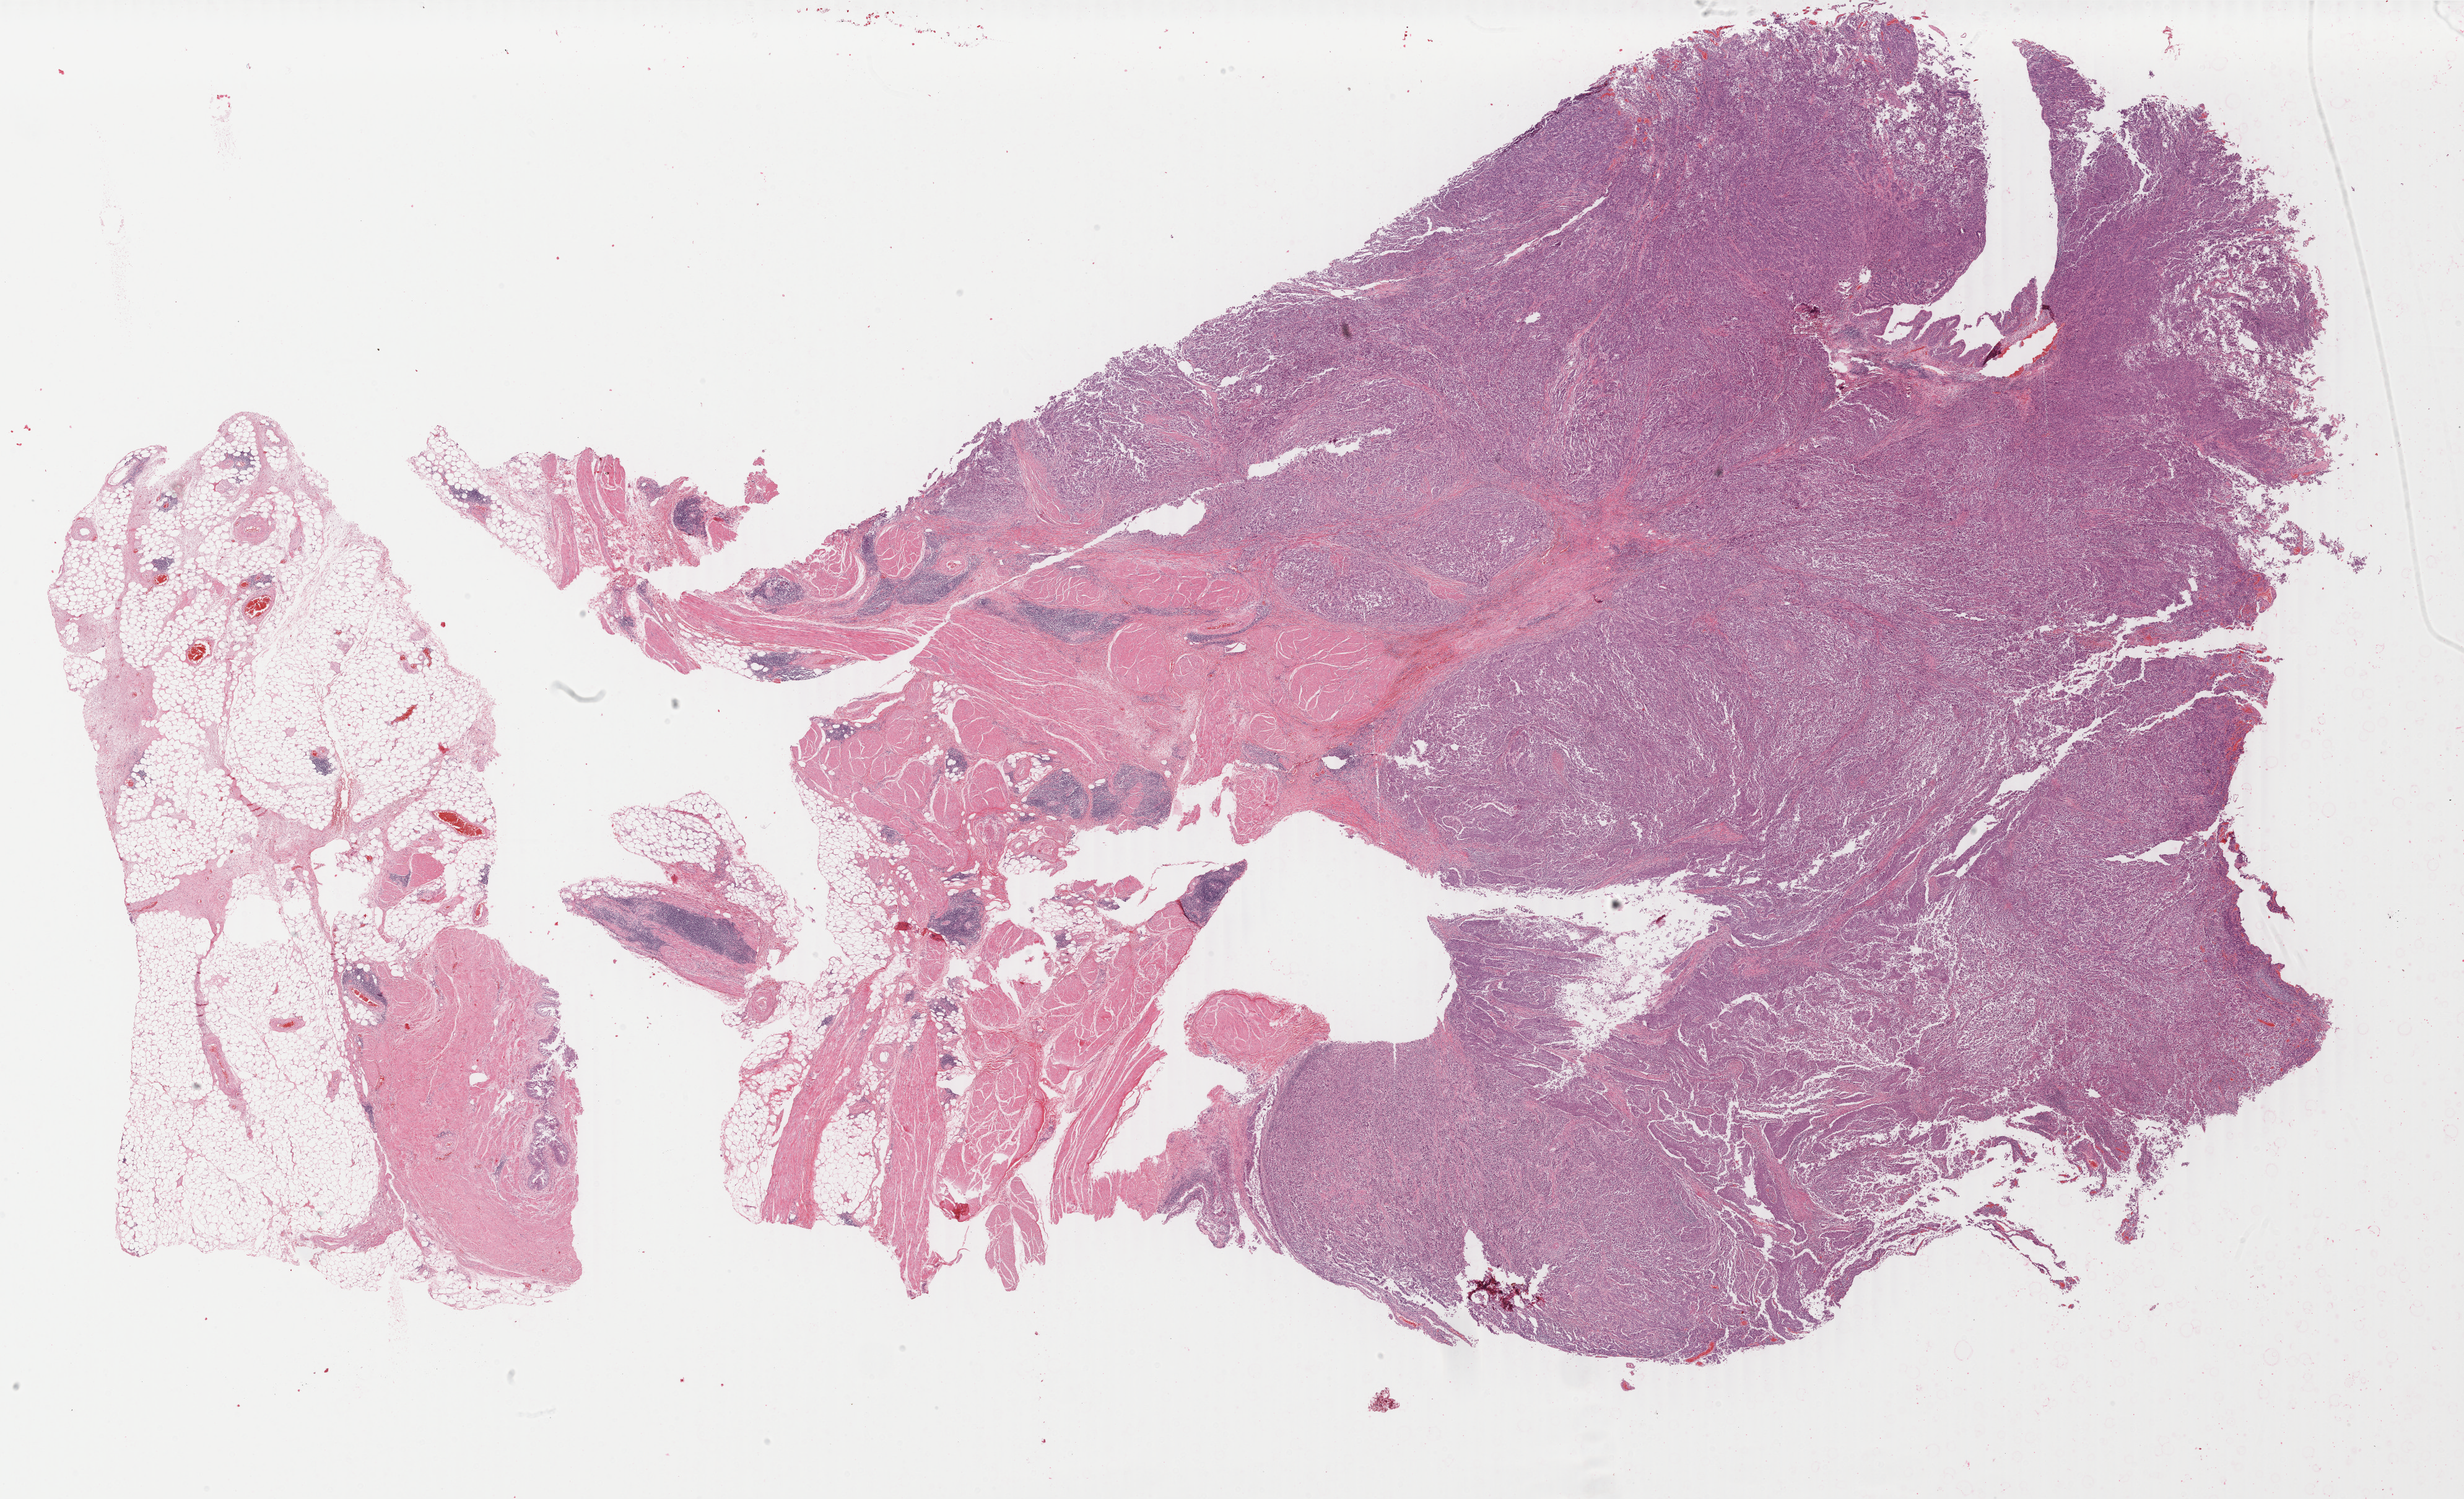
H&E-stained whole-slide image, low-resolution overview of the scanned area, about 31.6 x 19.2 mm; formalin-fixed paraffin-embedded (FFPE) diagnostic section; bladder, primary tumour sample. Patient: male, age at initial diagnosis 75 years. Histologic grade: high grade.
Histologic diagnosis: Papillary transitional cell carcinoma (posterior wall of bladder). AJCC pathologic stage: II.